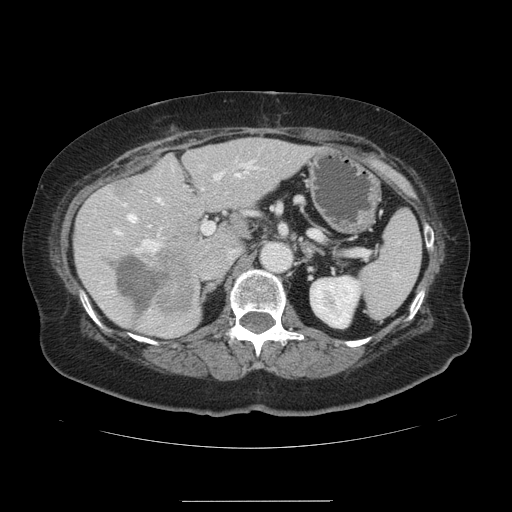
Contrast-enhanced abdominal CT, one axial slice; position 75 of 141 along the scan axis; 120 kVp; intravenous contrast given; soft-tissue window (W 400 / L 40 HU); 512 × 512 image matrix. Female patient, age 74 years. From the clinical record (not read from this slice): diagnosis: colorectal cancer liver metastases, imaged before liver resection; multiple liver metastases: yes; largest metastasis: 7 cm.
Outlined on this slice (manually delineated by an expert):
- hepatic veins: bounding box <128,173,239,228> (left, top, right, bottom; pixels)
- liver: <75,138,313,337>
- planned liver remnant (the part of the liver to remain after resection): <75,138,313,336>
- portal vein (with intrahepatic branches): <114,161,253,252>
- liver metastasis: <114,179,131,190>
- liver metastasis: <117,257,169,315>
- liver metastasis: <158,249,194,313>